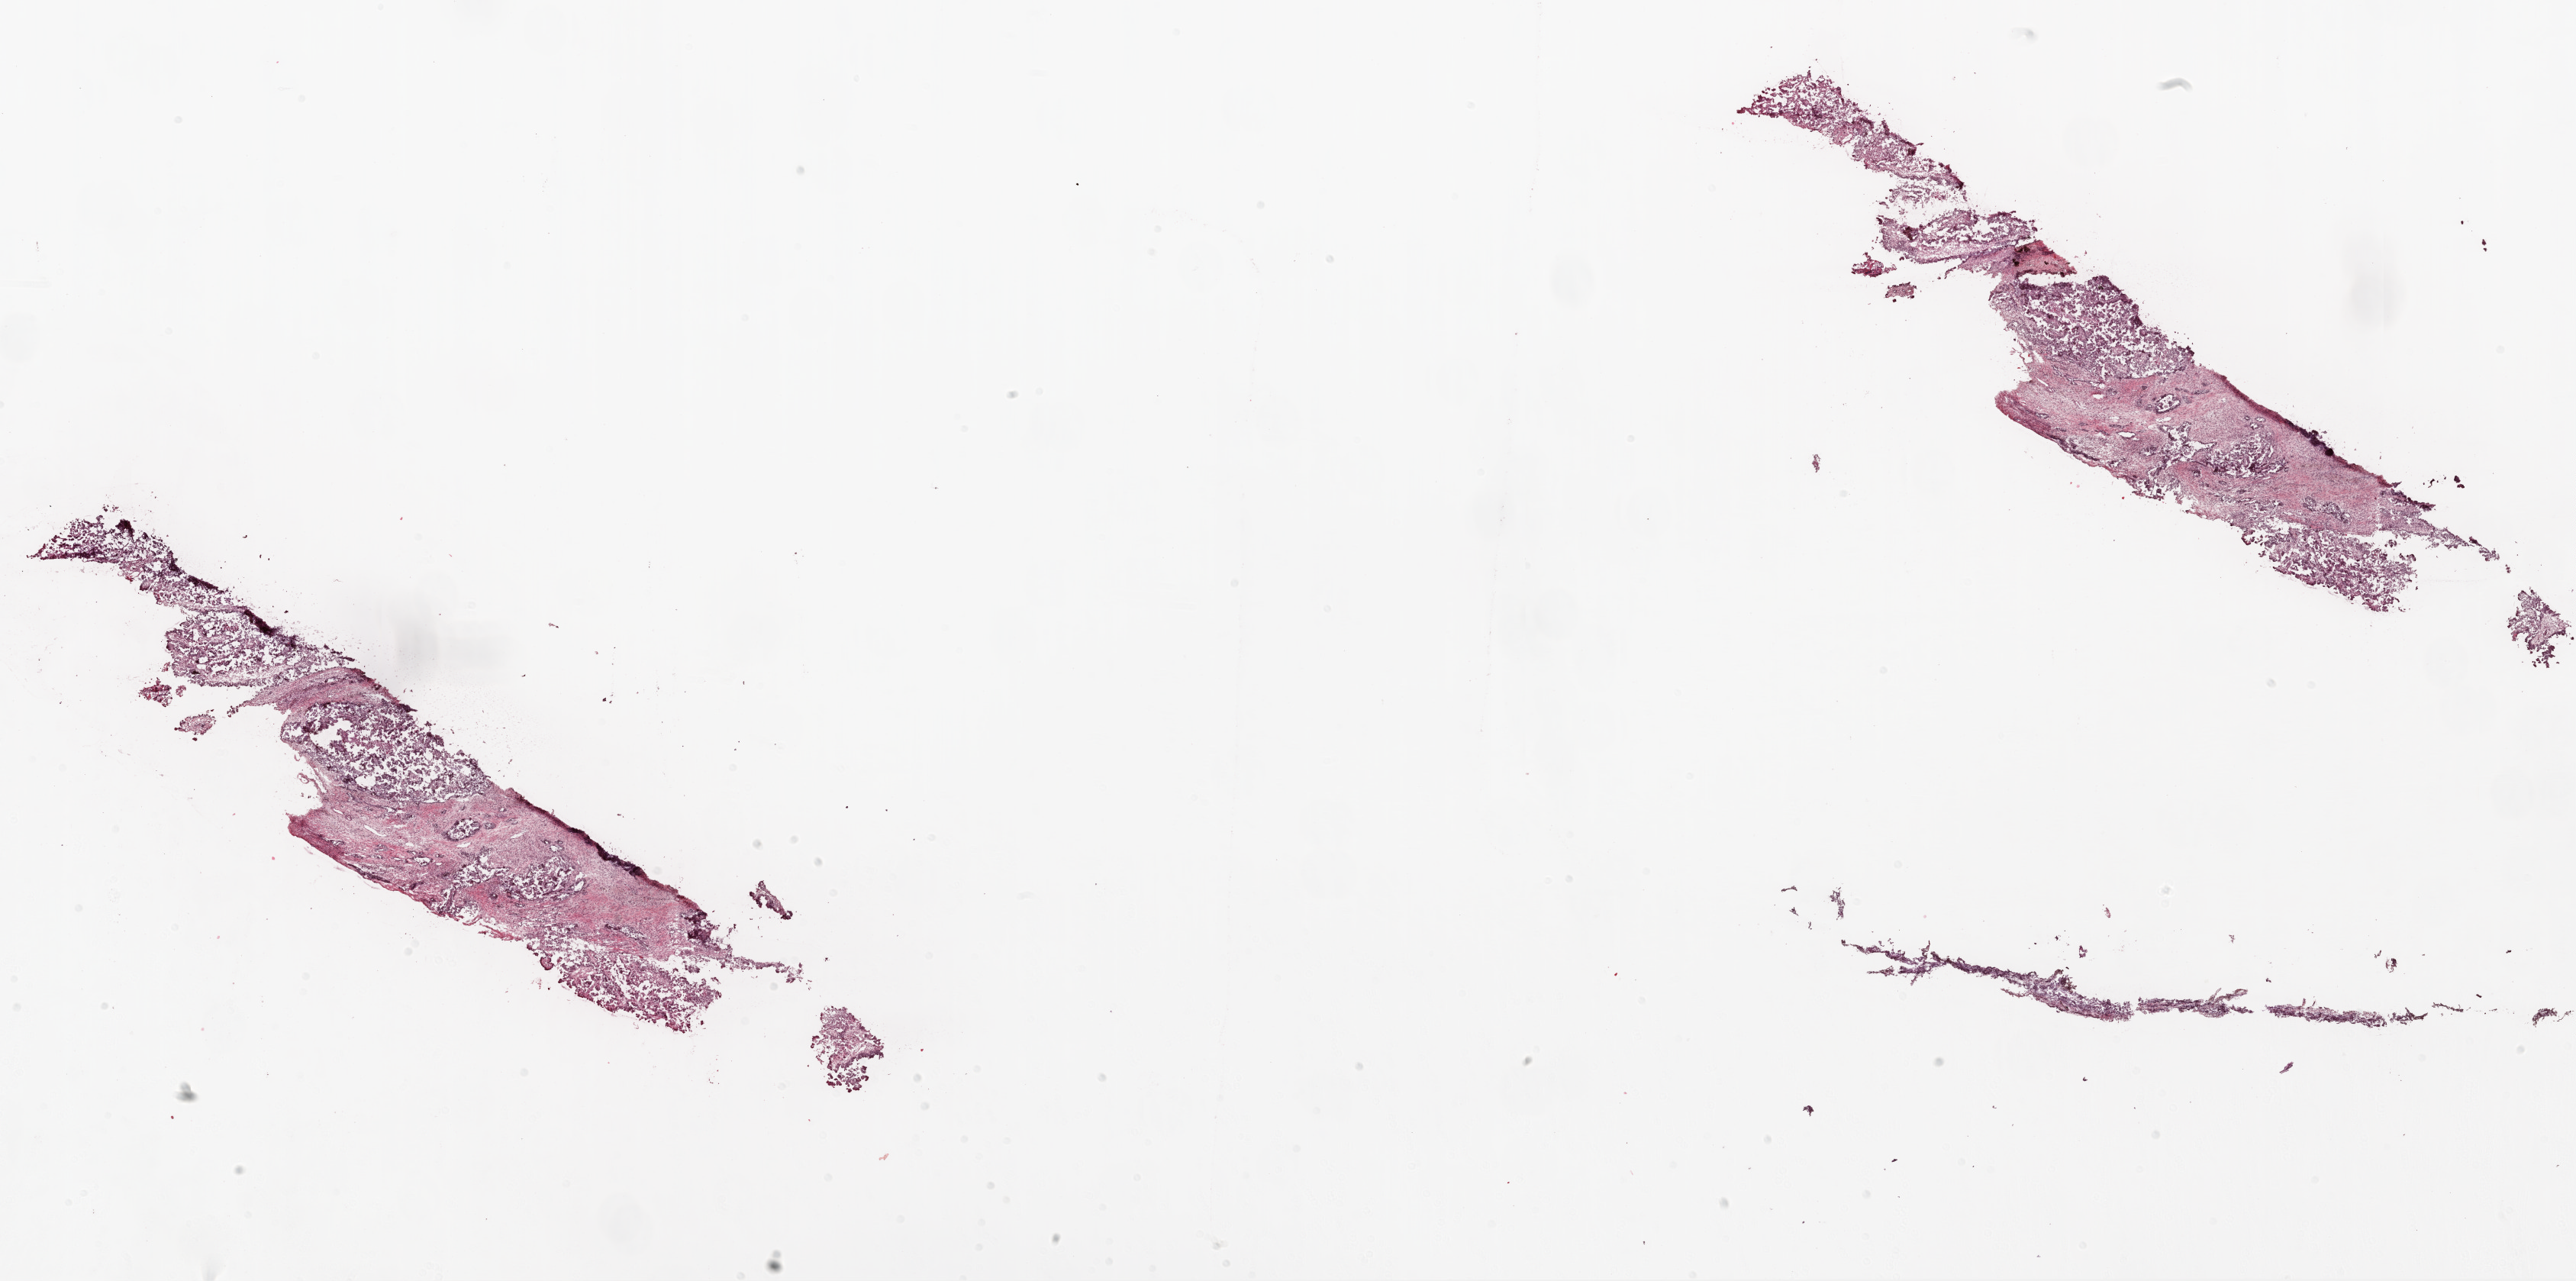
Whole-slide histology image, H&E — whole scanned area (about 27.1 x 13.5 mm, from a 20x scan) shown as a low-resolution overview, frozen section, sample: primary tumour, ovary. Female patient; age at initial diagnosis 44 years. Histologic grade: G3 (poorly differentiated). Pathologist review of this section (percent, as recorded): tumour cells 60%, tumour nuclei 90%, normal cells 0%, stromal cells 40%, necrosis 0%.
Histologic diagnosis: Serous cystadenocarcinoma, NOS. FIGO stage: IIIC. Laterality: bilateral.